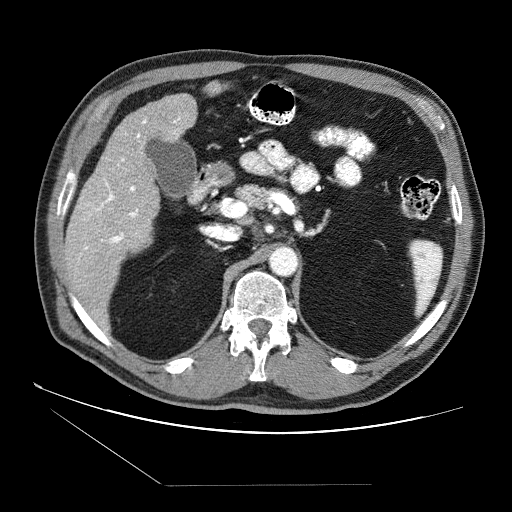
Contrast-enhanced abdominal CT (liver protocol), one axial slice. Slice 37 of 87 in the series (ordered by position). 120 kVp. Soft-tissue window (W 400 / L 40 HU). 512 × 512 image matrix, field of view 400 × 400 mm. From the clinical record (not read from this slice): diagnosis: hepatocellular carcinoma (patient treated with transarterial chemoembolisation; whether this scan precedes or follows treatment is not stated here); TNM stage (as recorded): Stage-II; Child-Pugh class: B; tumour differentiation: no biopsy; tumour size: 2.6 cm.
Outlined on this slice (semi-automatic segmentation, software-assisted and operator-edited):
- liver parenchyma outside the tumour (the mass and vessels are separate outlines, so this box may not span the whole liver): bounding box <64,81,223,320> (left, top, right, bottom; pixels)
- liver vessels: <72,116,181,304>